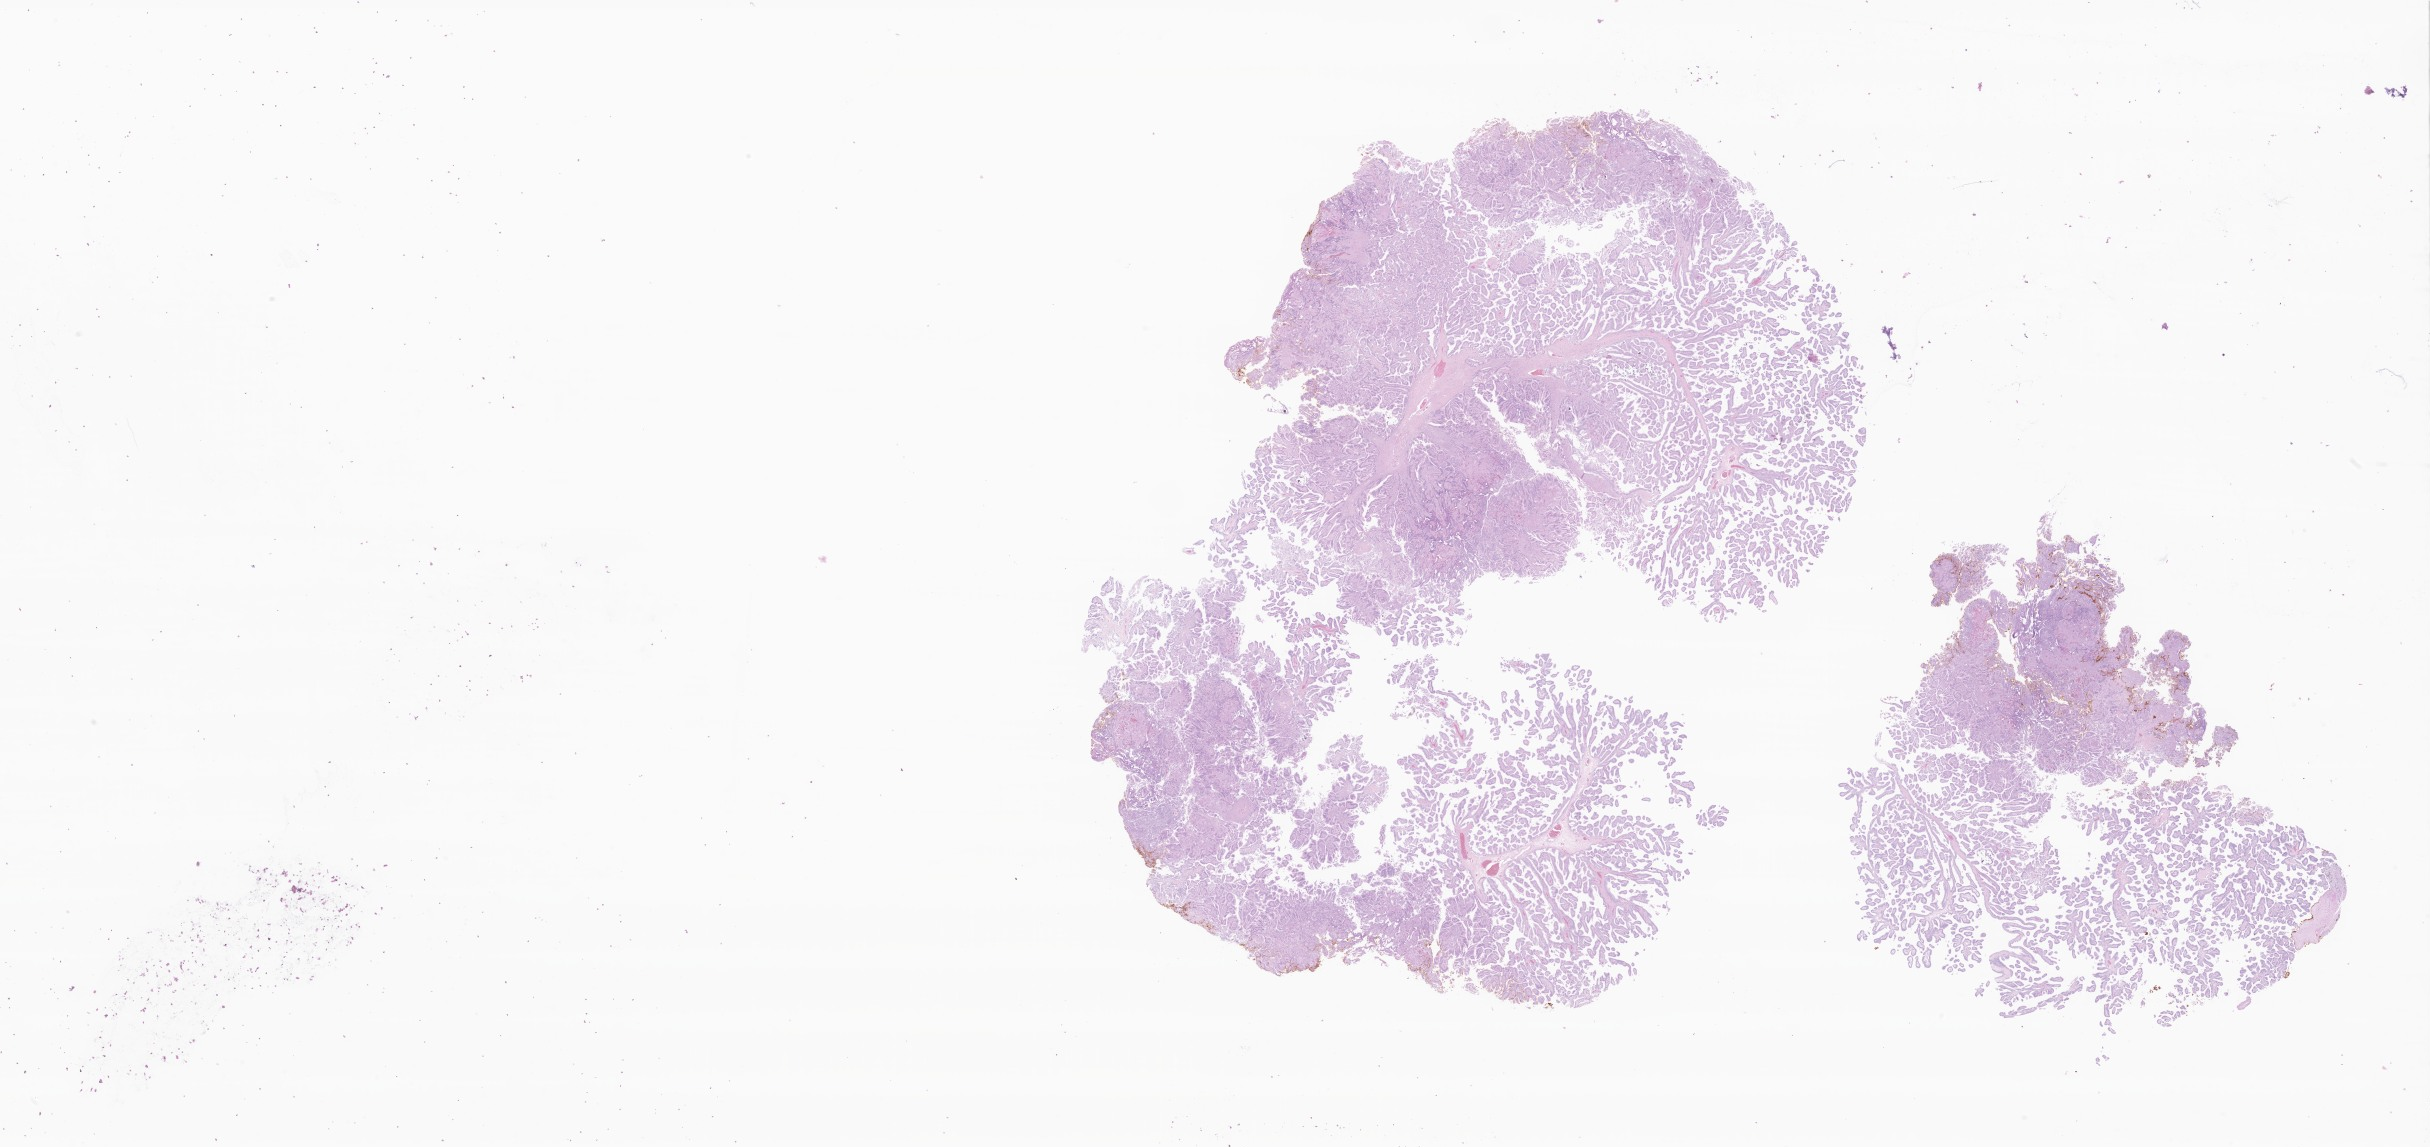
Whole-slide image, hematoxylin and eosin (H&E) stain of tumor tissue from the cerebral ventricle — shown as a low-resolution overview of the whole scanned area (about 41.0 x 19.3 mm), formalin-fixed paraffin-embedded section. Patient: male, age 115 months (9 years 7 months).
Diagnosis (ICD-O-3 morphology term): Choroid plexus papilloma, NOS.